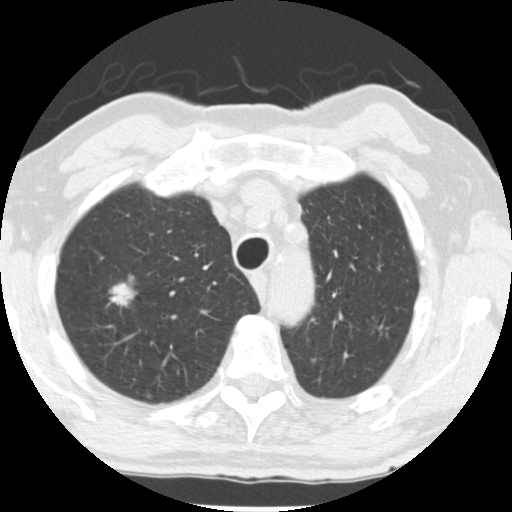
Axial slice from a low-dose chest CT screening exam. Baseline annual screen. Lung window (W 1500 / L -600 HU). Slice 202 of 252 in the series. Male participant, aged 69 years at enrolment.
- Expert reader's lesion annotation, bounding box [x1, y1, x2, y2] px = [91, 270, 151, 326].
- The screening reader recorded 2 non-calcified nodules or masses ≥4 mm on this exam (right upper lobe, left upper lobe); which of them this box marks is not recorded.
- Official screen result: positive, change unspecified: nodule(s) >= 4 mm or enlarging nodule(s), mass(es), or other non-specific abnormalities suspicious for lung cancer.